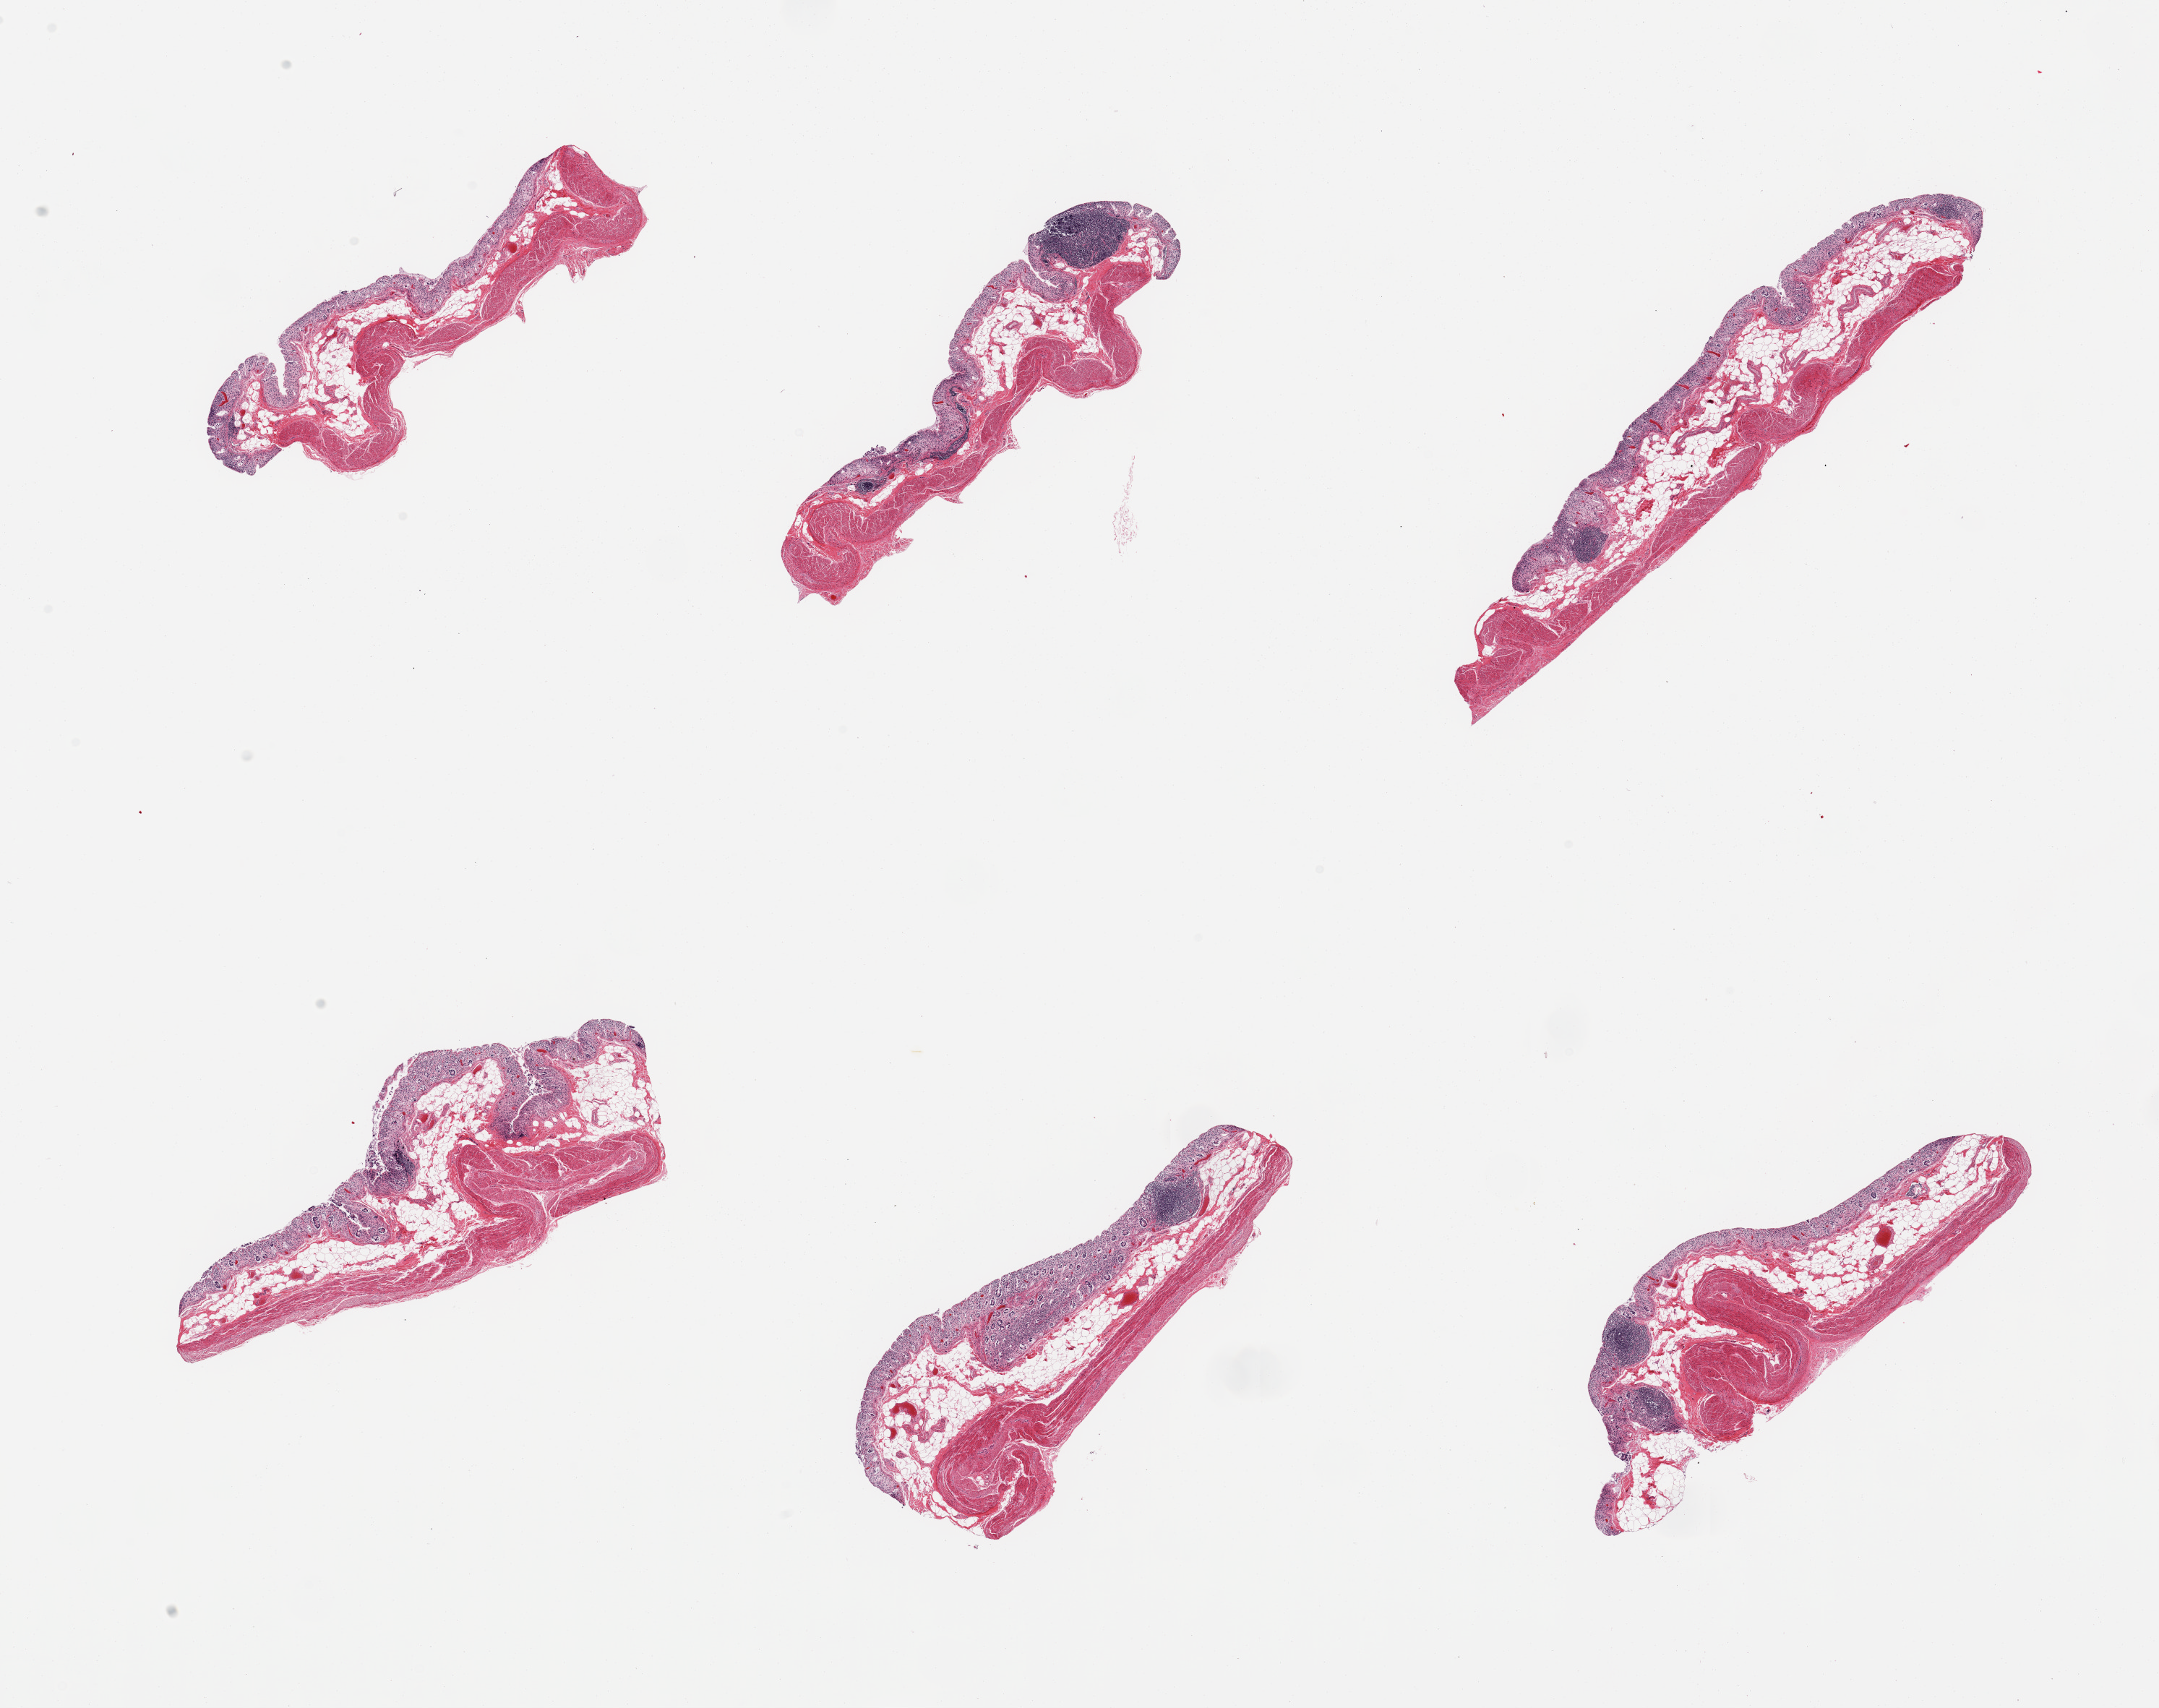
H&E whole-slide image, whole scanned area (about 23.6 x 18.7 mm, from a 20x scan) shown as a low-resolution overview, PAXgene-fixed, paraffin-embedded tissue, sampled site (target tissue): transverse colon, donor tissue sample. Female donor.
Reviewer comment on this tissue sample: 6 pieces, mucosa completely autolyzed/sloughed.